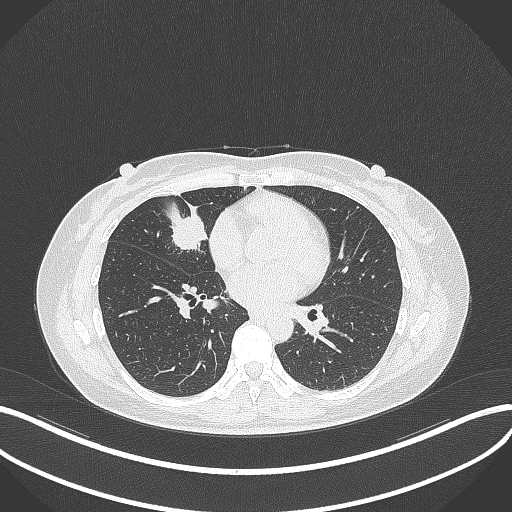
Chest CT, one axial slice; position 132 of 284 along the scan axis; 120 kVp; lung window (W 1500 / L -600 HU); 1 mm slice thickness; 512 × 512 image matrix, field of view 400 × 400 mm. Patient: female, 43 years. Case-level facts recorded for this patient, not image findings: clinical TNM (as recorded): T1c N3 M1; histopathological grade: G1.
Outlined on this slice (rectangle marked by the reading radiologist):
- lung tumour (recorded histology: adenocarcinoma): bounding box [x1, y1, x2, y2] px = [165, 205, 209, 257]